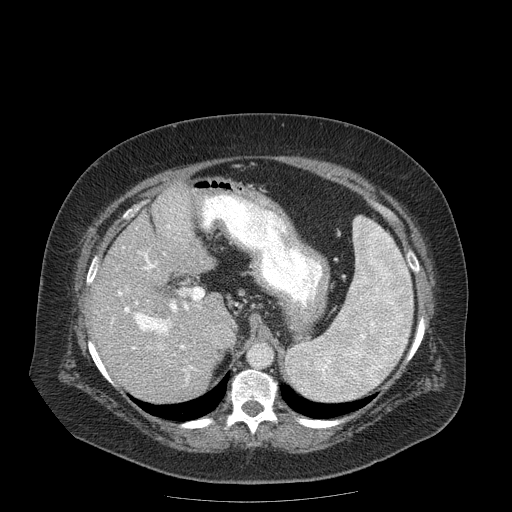
Contrast-enhanced abdominal CT (liver protocol), one axial slice. Position 117 of 204 along the scan axis. Reconstruction kernel STANDARD. 120 kVp. Soft-tissue window (W 400 / L 40 HU). 512 × 512 image matrix. From the clinical record (not read from this slice): diagnosis: hepatocellular carcinoma (patient treated with transarterial chemoembolisation; whether this scan precedes or follows treatment is not stated here); TNM stage (as recorded): Stage-IIIB.
Annotated regions visible in this slice (semi-automatically segmented with operator editing):
- abdominal aorta: box from (x=249, y=344) to (x=272, y=367) px
- liver parenchyma outside the tumour (the mass and vessels are separate outlines, so this box may not span the whole liver): (x=90, y=182)–(x=232, y=402)
- liver vessels: (x=111, y=208)–(x=202, y=382)